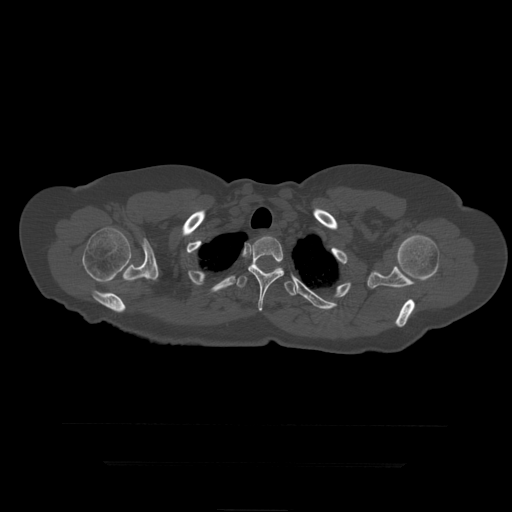
CT including the spine, one axial slice. Slice 361 of 399 in the series (ordered by position). Reconstruction kernel STANDARD. 120 kVp. Bone window (W 1800 / L 400 HU). 1.25 mm slice thickness. 512 × 512 image matrix, field of view 450 × 450 mm. Patient age 41 years. Case-level facts recorded for this patient, not image findings: primary cancer: breast.
Outlined on this slice (semi-automatically segmented with operator editing):
- T3 vertebra: bounding box (x1, y1, x2, y2) in pixels: (248, 236, 285, 312)
- T4 vertebra: (237, 264, 298, 296)